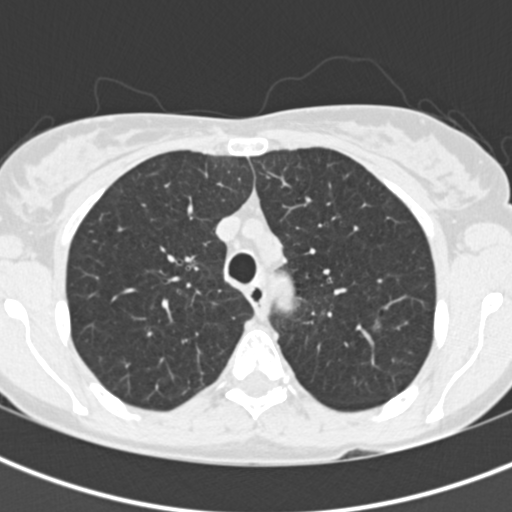
Chest CT (low-dose screening protocol), one axial image. First (baseline) screen. Lung window (W 1500 / L -600 HU). Standard (soft-tissue) reconstruction kernel (B30f). Female, age 56 years at enrolment. Current smoker at enrolment.
Lesion marked by an expert reader, bounding box [x1, y1, x2, y2] px = [364, 305, 400, 345]. Reader record for this screening exam (exam-level; its link to the box is not recorded): non-calcified nodule or mass ≥4 mm, right upper lobe, 6 × 5 mm, poorly defined margins, ground glass attenuation. Note: the box lies in the patient's left hemithorax on this image, whereas the reader's record names the right lung; they may be different findings.